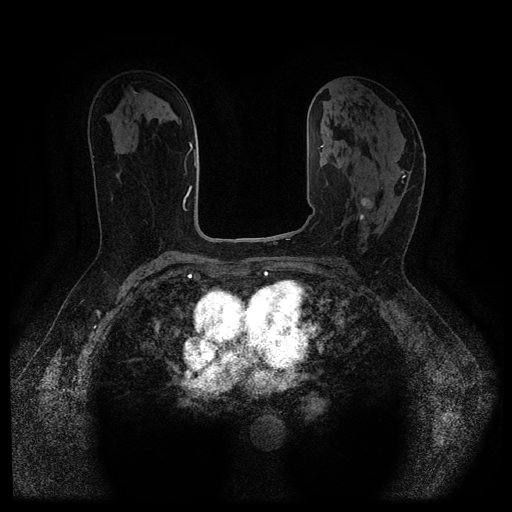
Breast MRI (dynamic contrast-enhanced, multi-phase), one axial slice; slice 59 of 116 in the series (ordered by position); dynamic contrast-enhanced series, time point 2 of 5 at this slice position (early post-contrast); 1.5 T; TE 2.6 ms, TR 5.4 ms; 2 mm slice thickness; 512 × 512 image matrix. Female patient, age 64 years.
Outlined on this slice (semi-automatically segmented with operator editing):
- breast lesion (labelled 'tumour' in the annotation; benign lesions carry a separate 'benign' label): bounding box (x1, y1, x2, y2) in pixels: (357, 197, 373, 210)